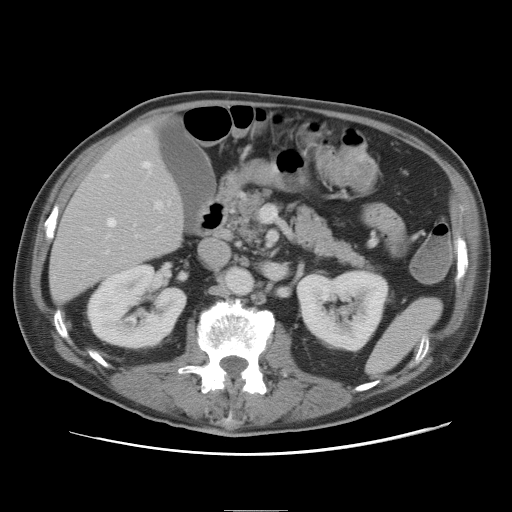
Contrast-enhanced abdominal CT, one axial slice. Slice 32 of 89 in the series (ordered by position). Intravenous contrast given. Soft-tissue window (W 400 / L 40 HU). 5 mm slice thickness. 512 × 512 image matrix, field of view 375 × 375 mm. Male patient, age 69 years. Case-level facts recorded for this patient, not image findings: diagnosis: colorectal cancer liver metastases, imaged before liver resection; multiple liver metastases: no; largest metastasis: 8.5 cm; disease in both lobes: no.
Outlined on this slice (expert manual segmentation):
- hepatic veins: box from (x=105, y=161) to (x=152, y=227) px
- liver: (x=50, y=126)–(x=183, y=303)
- planned liver remnant (the part of the liver to remain after resection): (x=50, y=126)–(x=183, y=303)
- portal vein (with intrahepatic branches): (x=106, y=200)–(x=163, y=253)